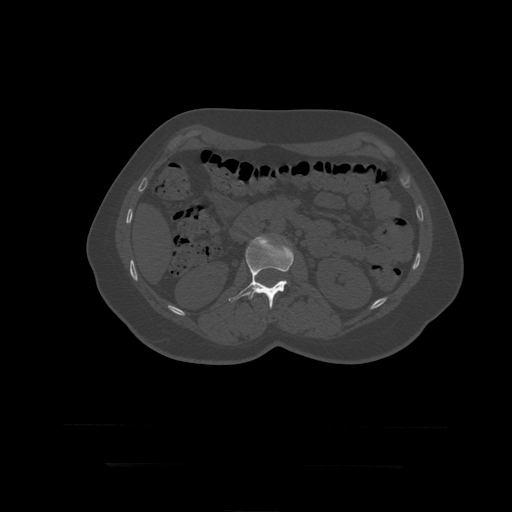
CT including the spine, one axial slice; position 147 of 399 along the scan axis; bone window (W 1800 / L 400 HU); 512 × 512 image matrix, field of view 450 × 450 mm. Patient age 41 years. Case-level facts recorded for this patient, not image findings: primary cancer: breast.
Annotated regions visible in this slice (semi-automatically segmented with operator editing):
- L2 vertebra: bounding box (x1, y1, x2, y2) in pixels: (229, 235, 294, 309)